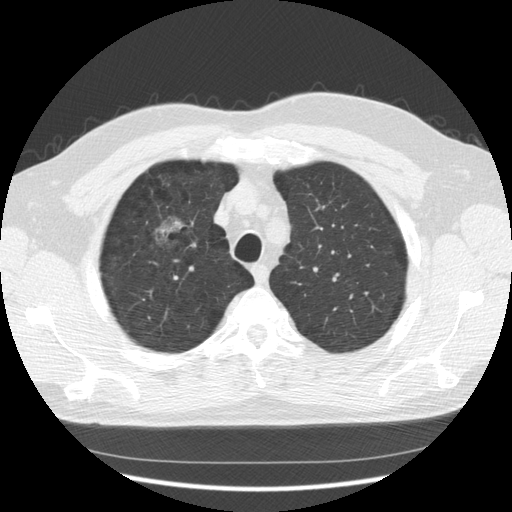
Chest CT (low-dose screening protocol), one axial image. Third annual screen. Lung window (W 1500 / L -600 HU). 2.5 mm slice thickness. Slice 100 of 133 in the series. 512 × 512 image matrix. Male participant, aged 60 years at enrolment.
Expert-annotated lung lesion, bounding box (x1, y1, x2, y2) in pixels: (142, 206, 198, 265). The exam's reader record, not a measurement of the box and not confirmed to be the same lesion: non-calcified nodule or mass ≥4 mm, right upper lobe, poorly defined margins, mixed attenuation, pre-existing on the prior screen: yes; interval growth: yes. Later outcome: lung cancer diagnosed 121 days after this screen — papillary adenocarcinoma, NOS, right upper lobe, moderately differentiated (G2), stage IB (AJCC 6th edition), 32 mm at pathology.